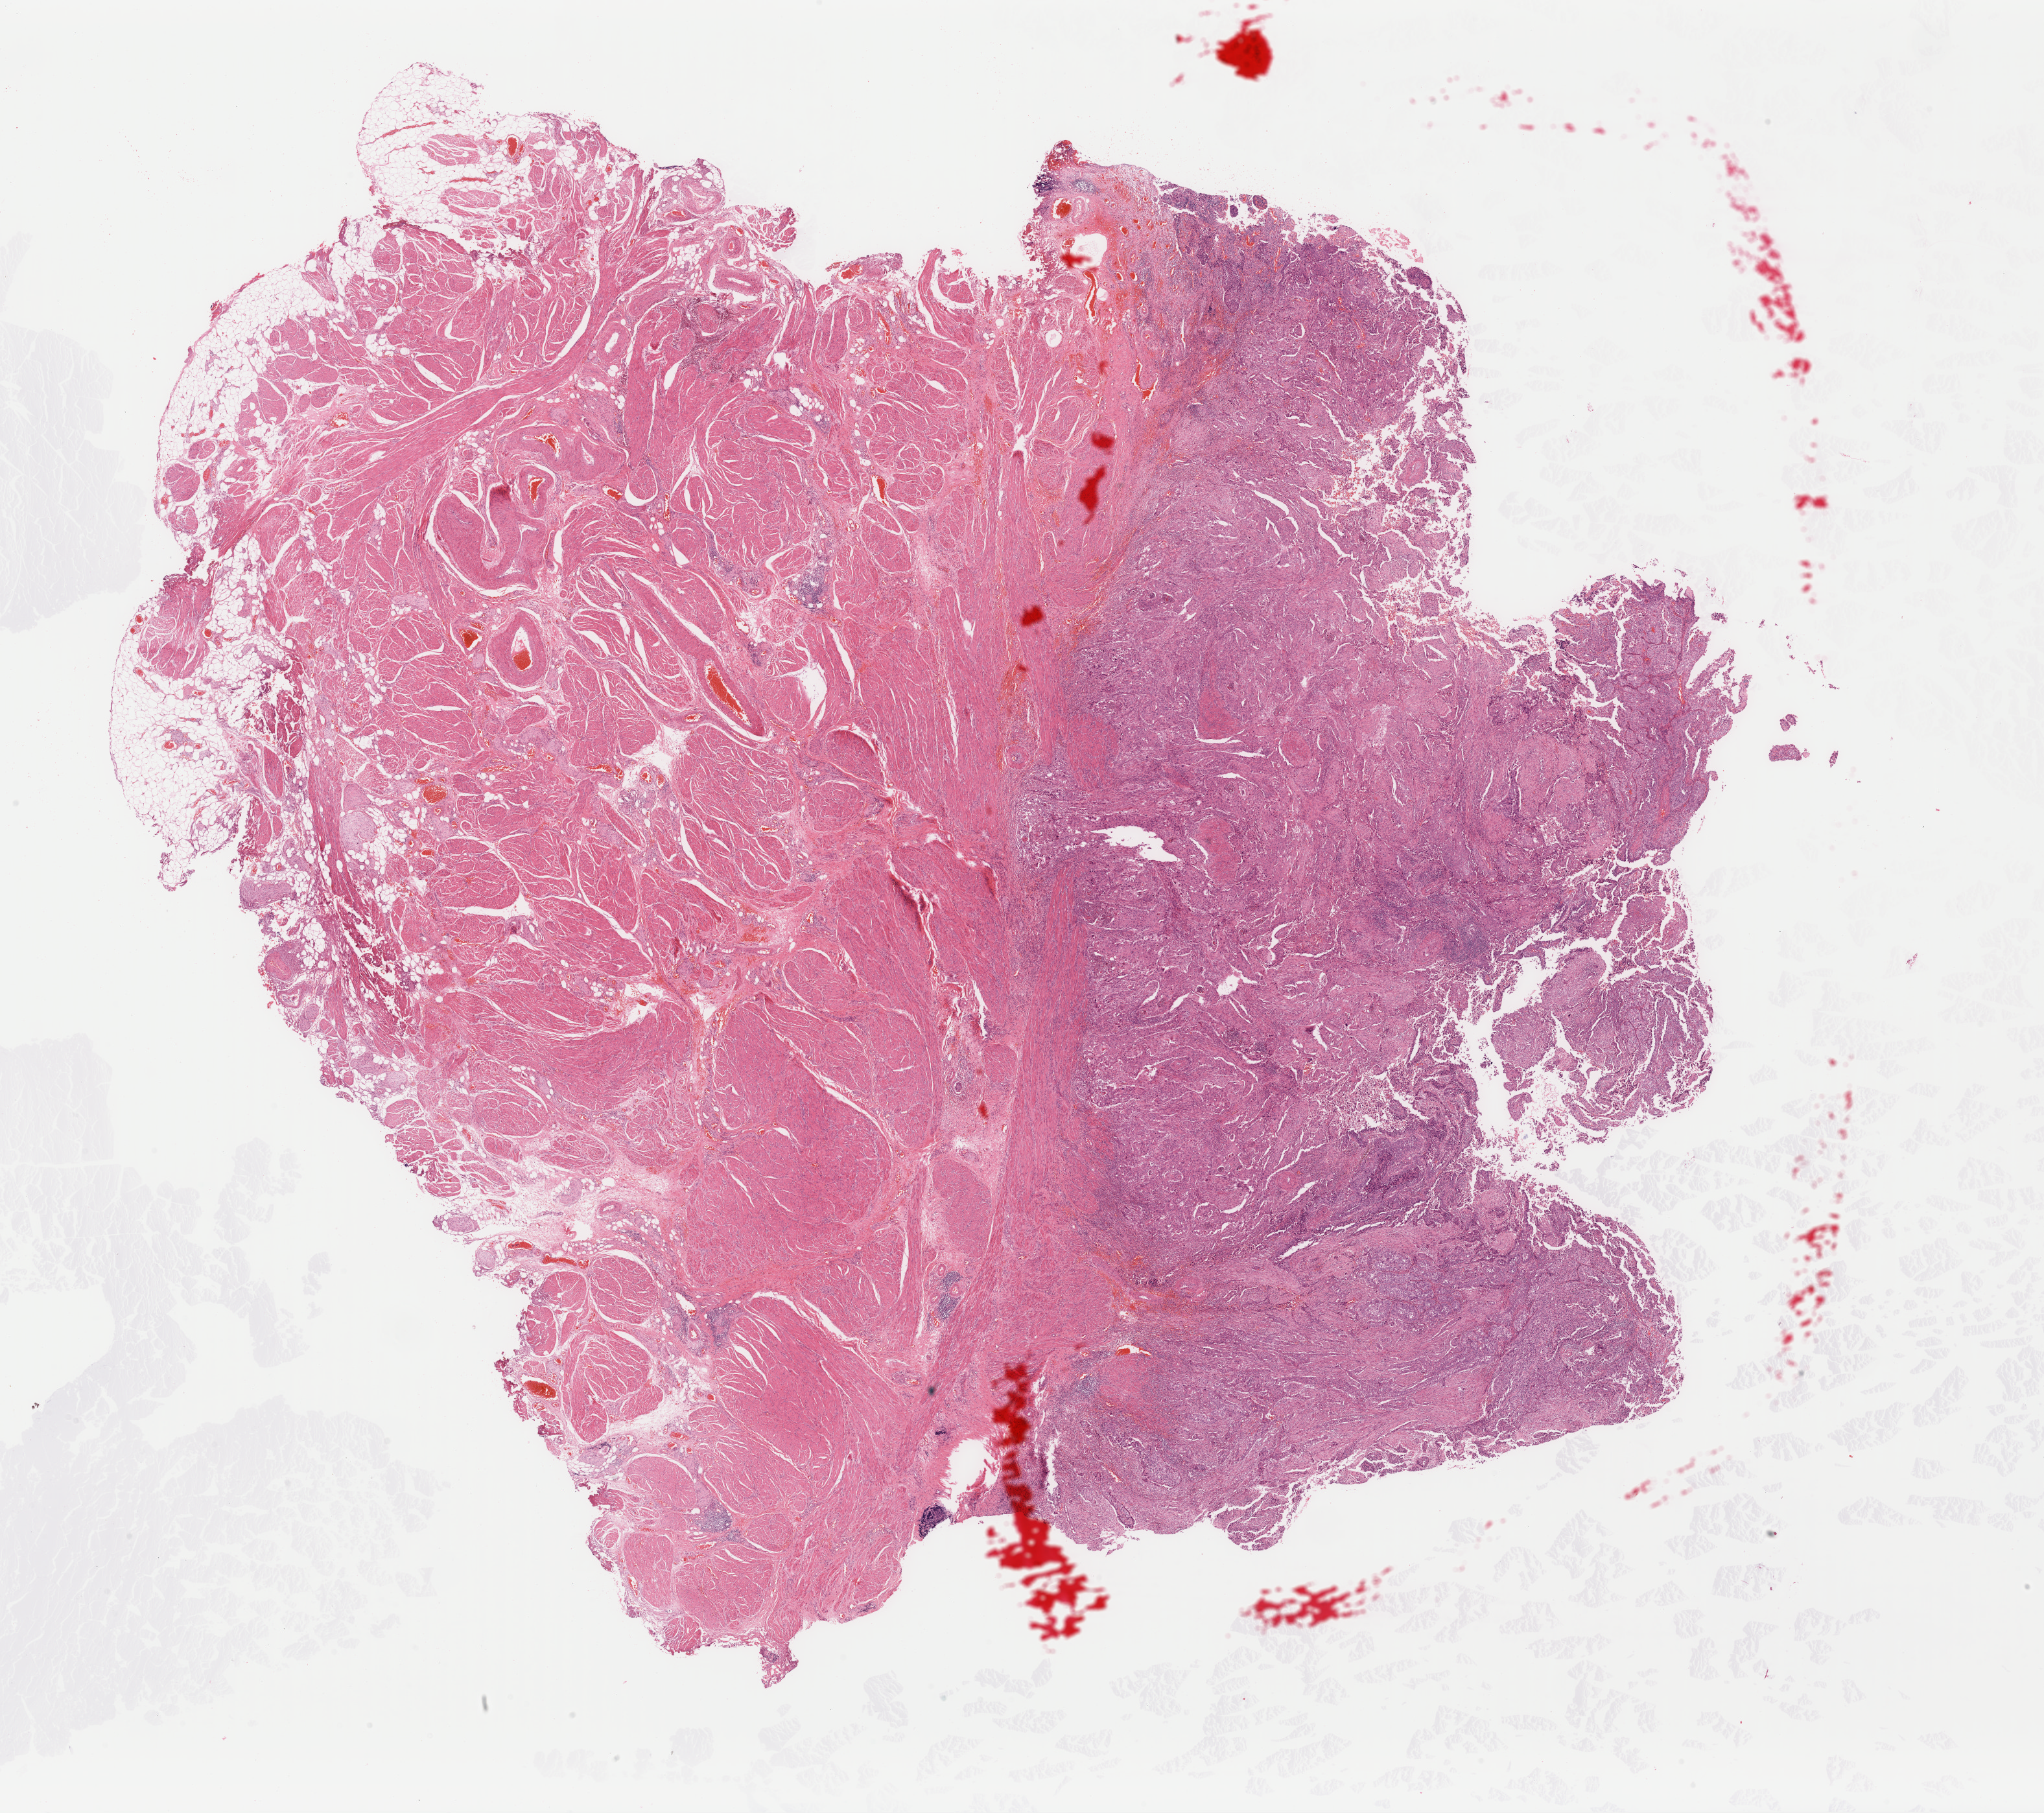
Digitized Hematoxylin and eosin (H&E) stained tissue section (whole slide) — shown as a low-resolution overview of the whole scanned area (about 24.9 x 22.1 mm, from a 40x scan), formalin-fixed paraffin-embedded (FFPE) diagnostic section, primary tumour sample from the bladder. Patient: male, age at initial diagnosis 56 years. Histologic grade: high grade.
AJCC pathologic stage: II (7th edition). TNM: T2b NX M0. Histologic diagnosis: Papillary transitional cell carcinoma.